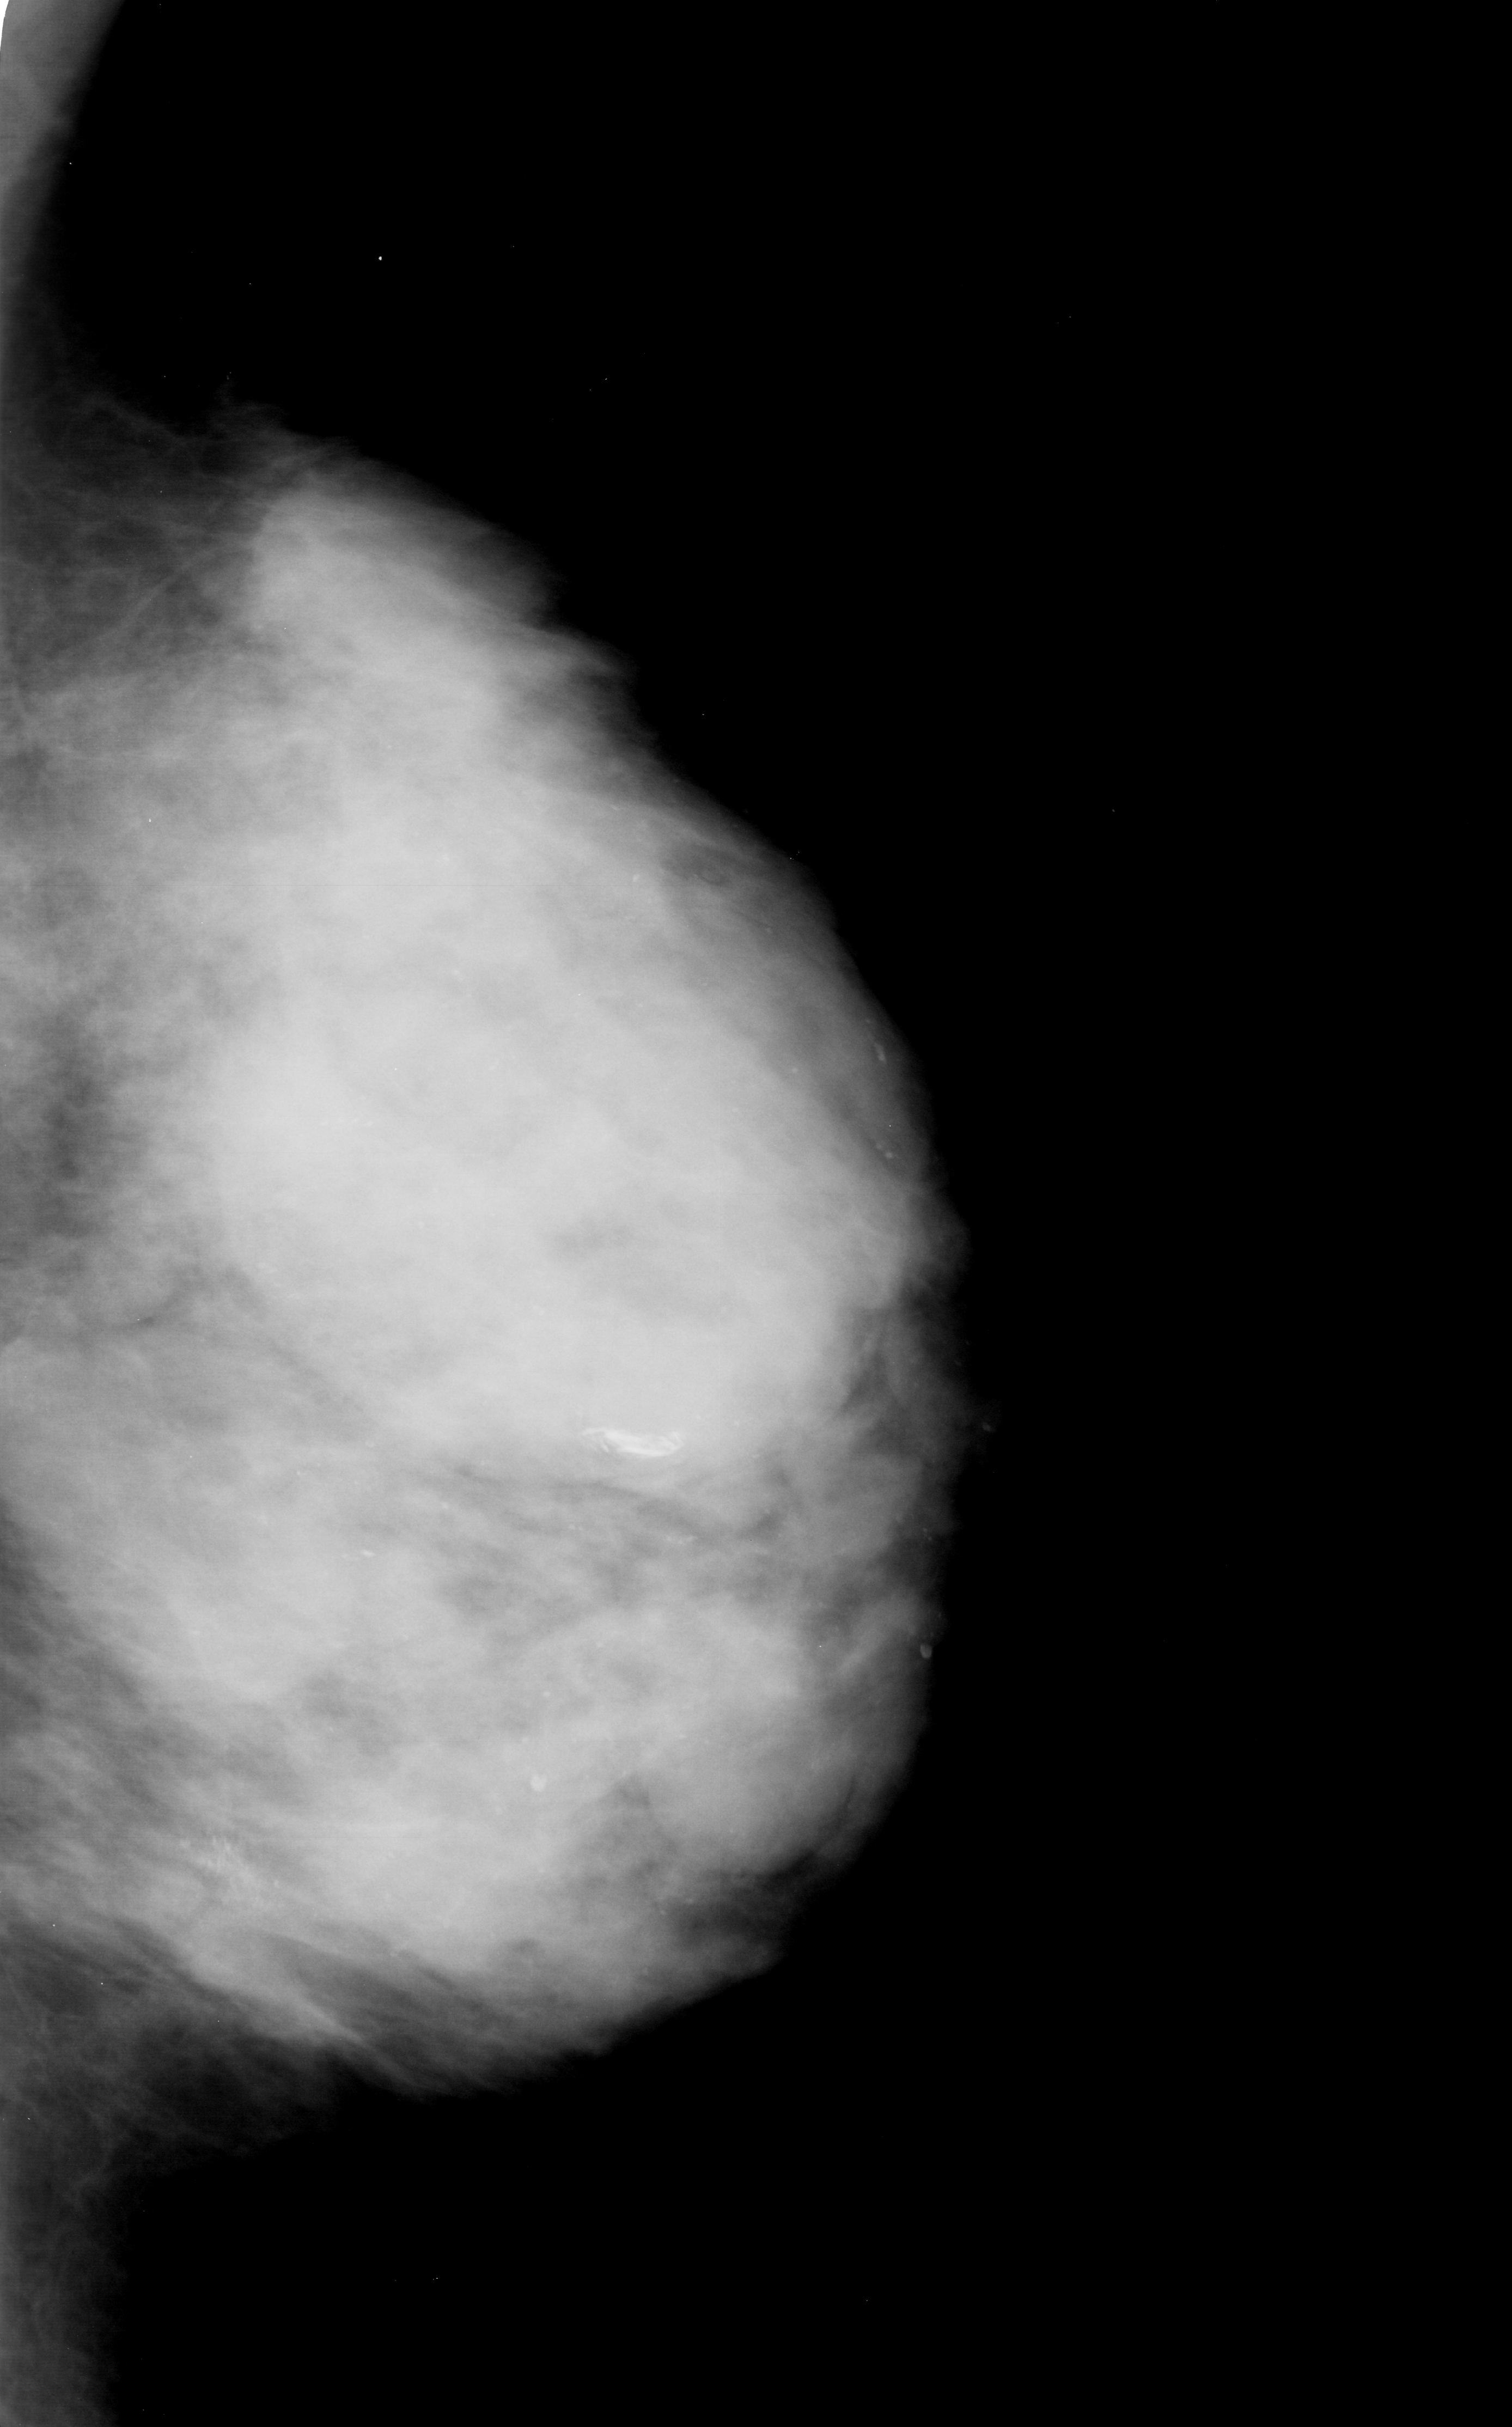
Digitized screen-film mammogram, left breast, mediolateral oblique (MLO) view, BI-RADS breast density category 4 (scale 1–4).
- Radiologist-marked abnormalities on this image: mass, shape round, margins circumscribed; BI-RADS assessment category 3; subtlety rating 3 on a 1 (subtle) to 5 (obvious) scale; pathology (as recorded): benign.